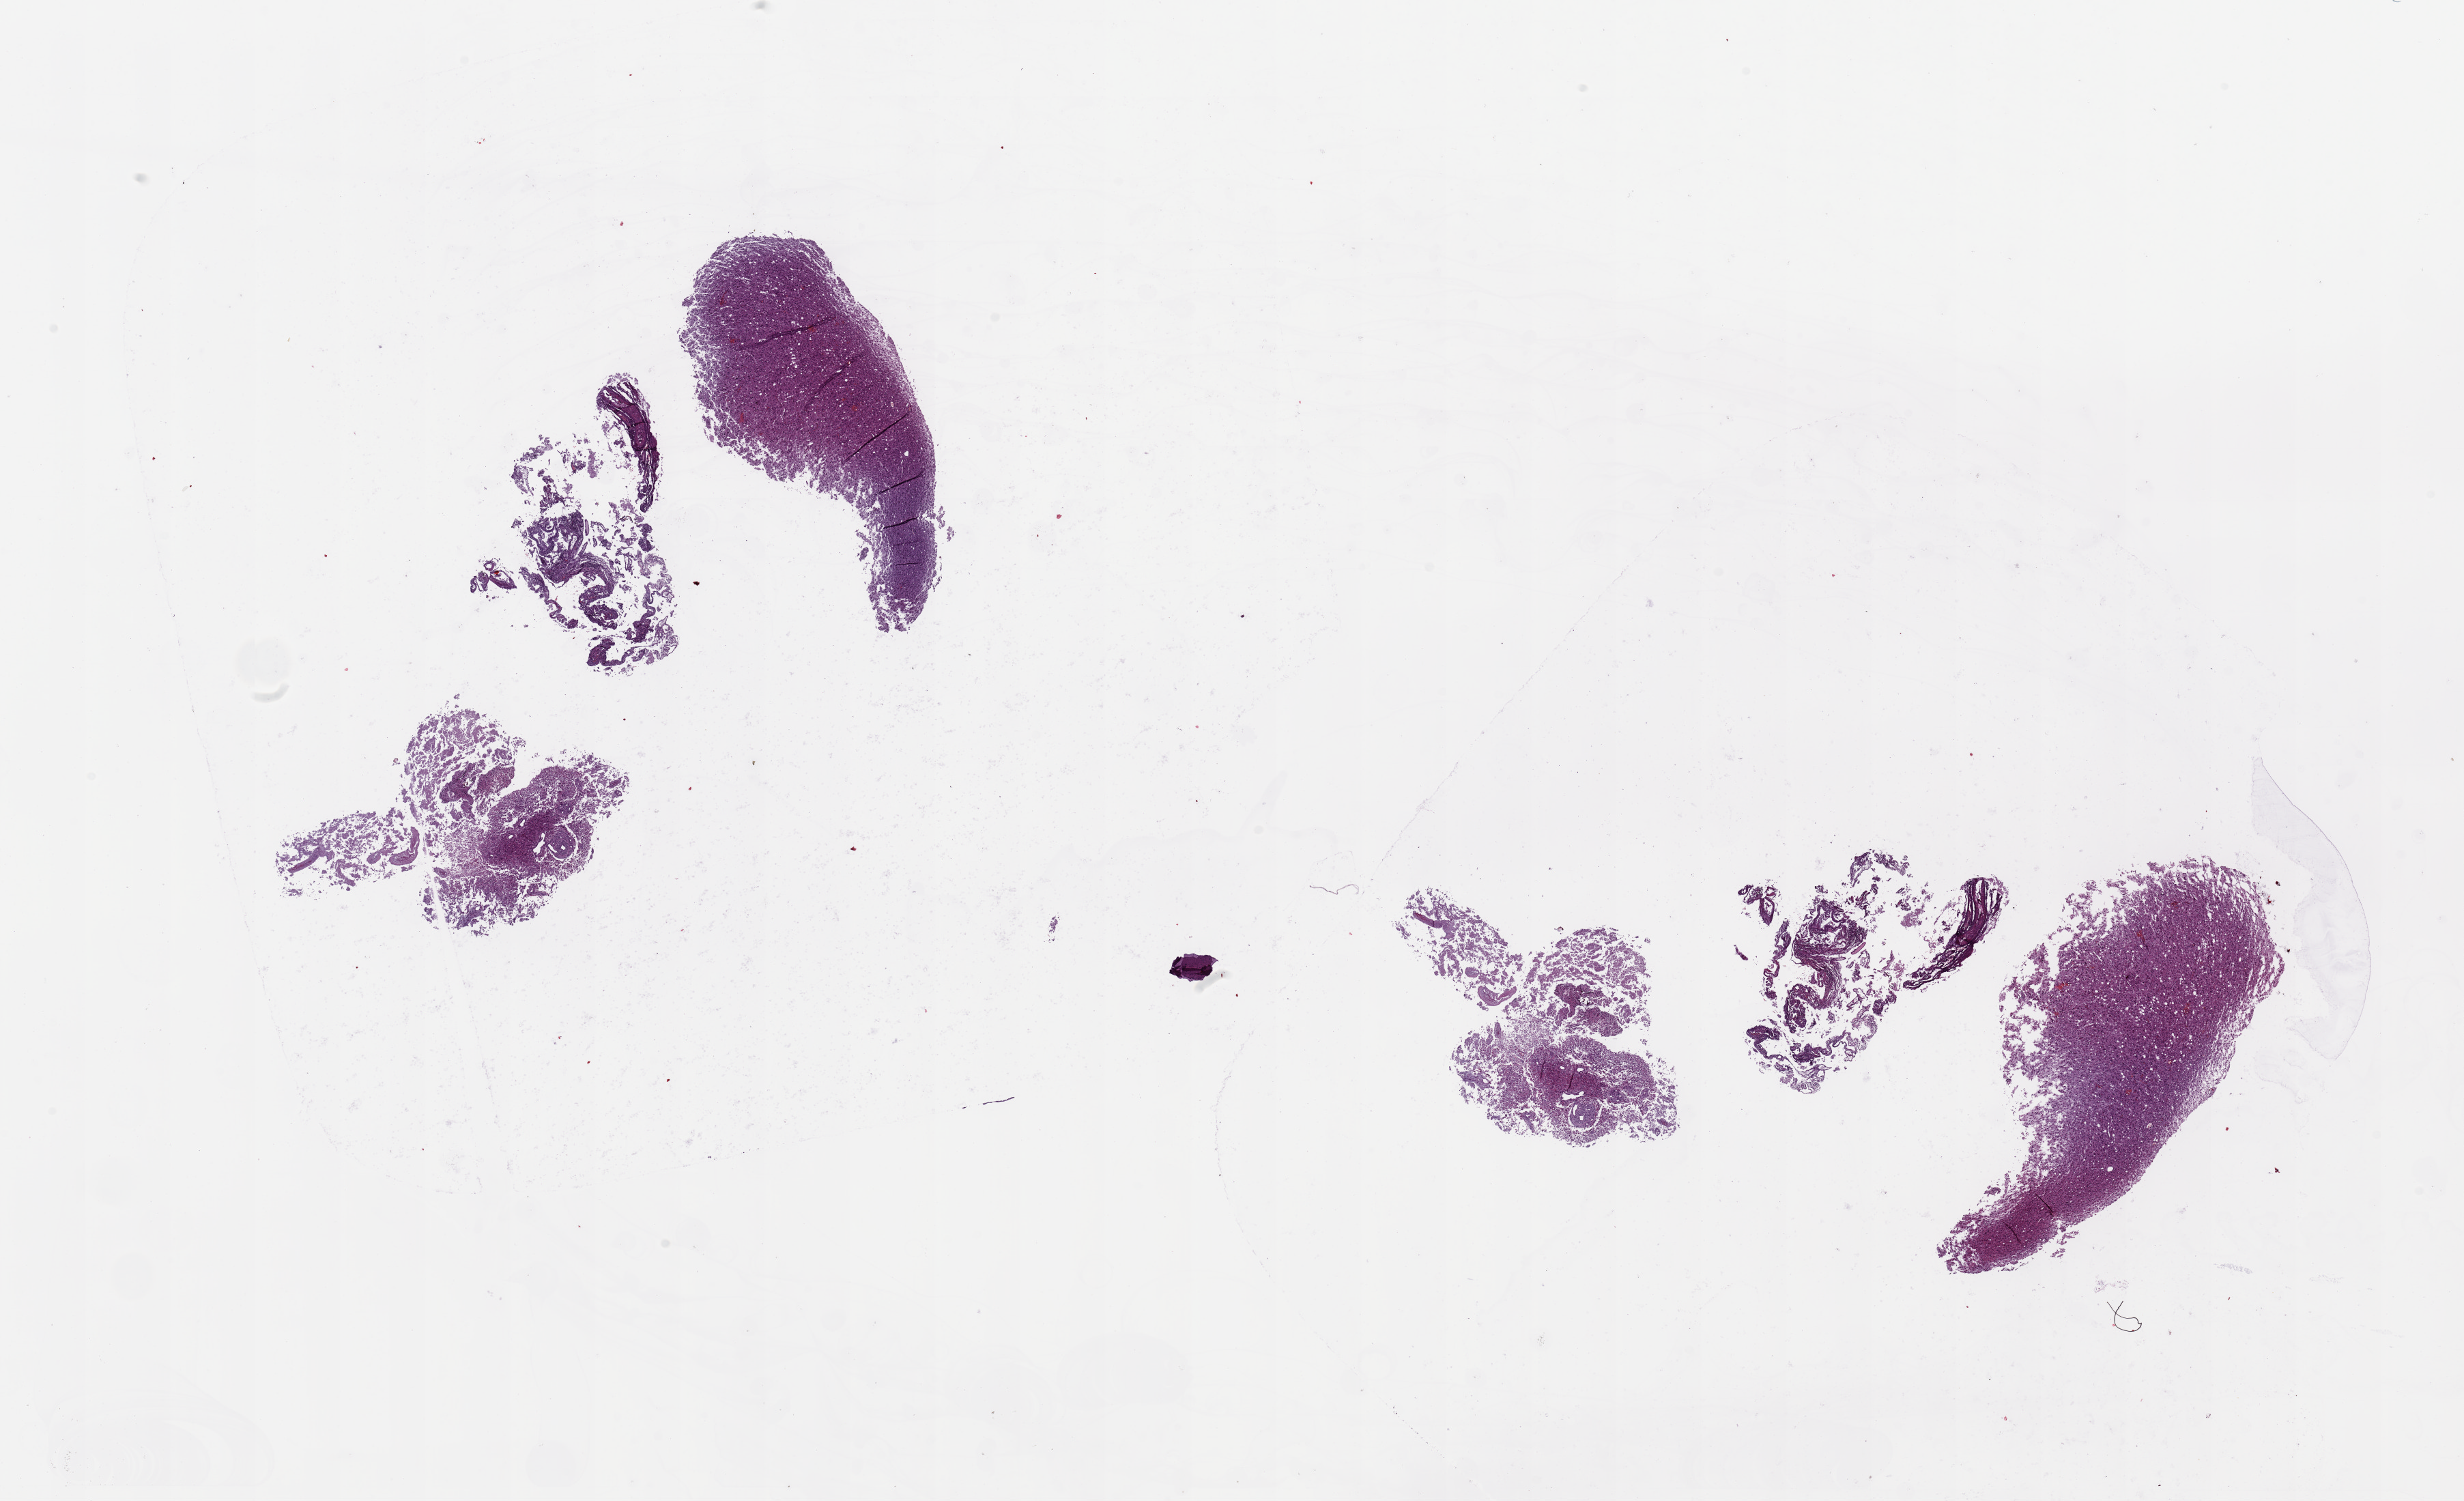
Hematoxylin and eosin (H&E) stained whole-slide image — low-resolution overview of the scanned area, about 28.5 x 17.4 mm, tumour tissue sample, brain. Patient: male, age 53 years.
* diagnosis: Glioblastoma